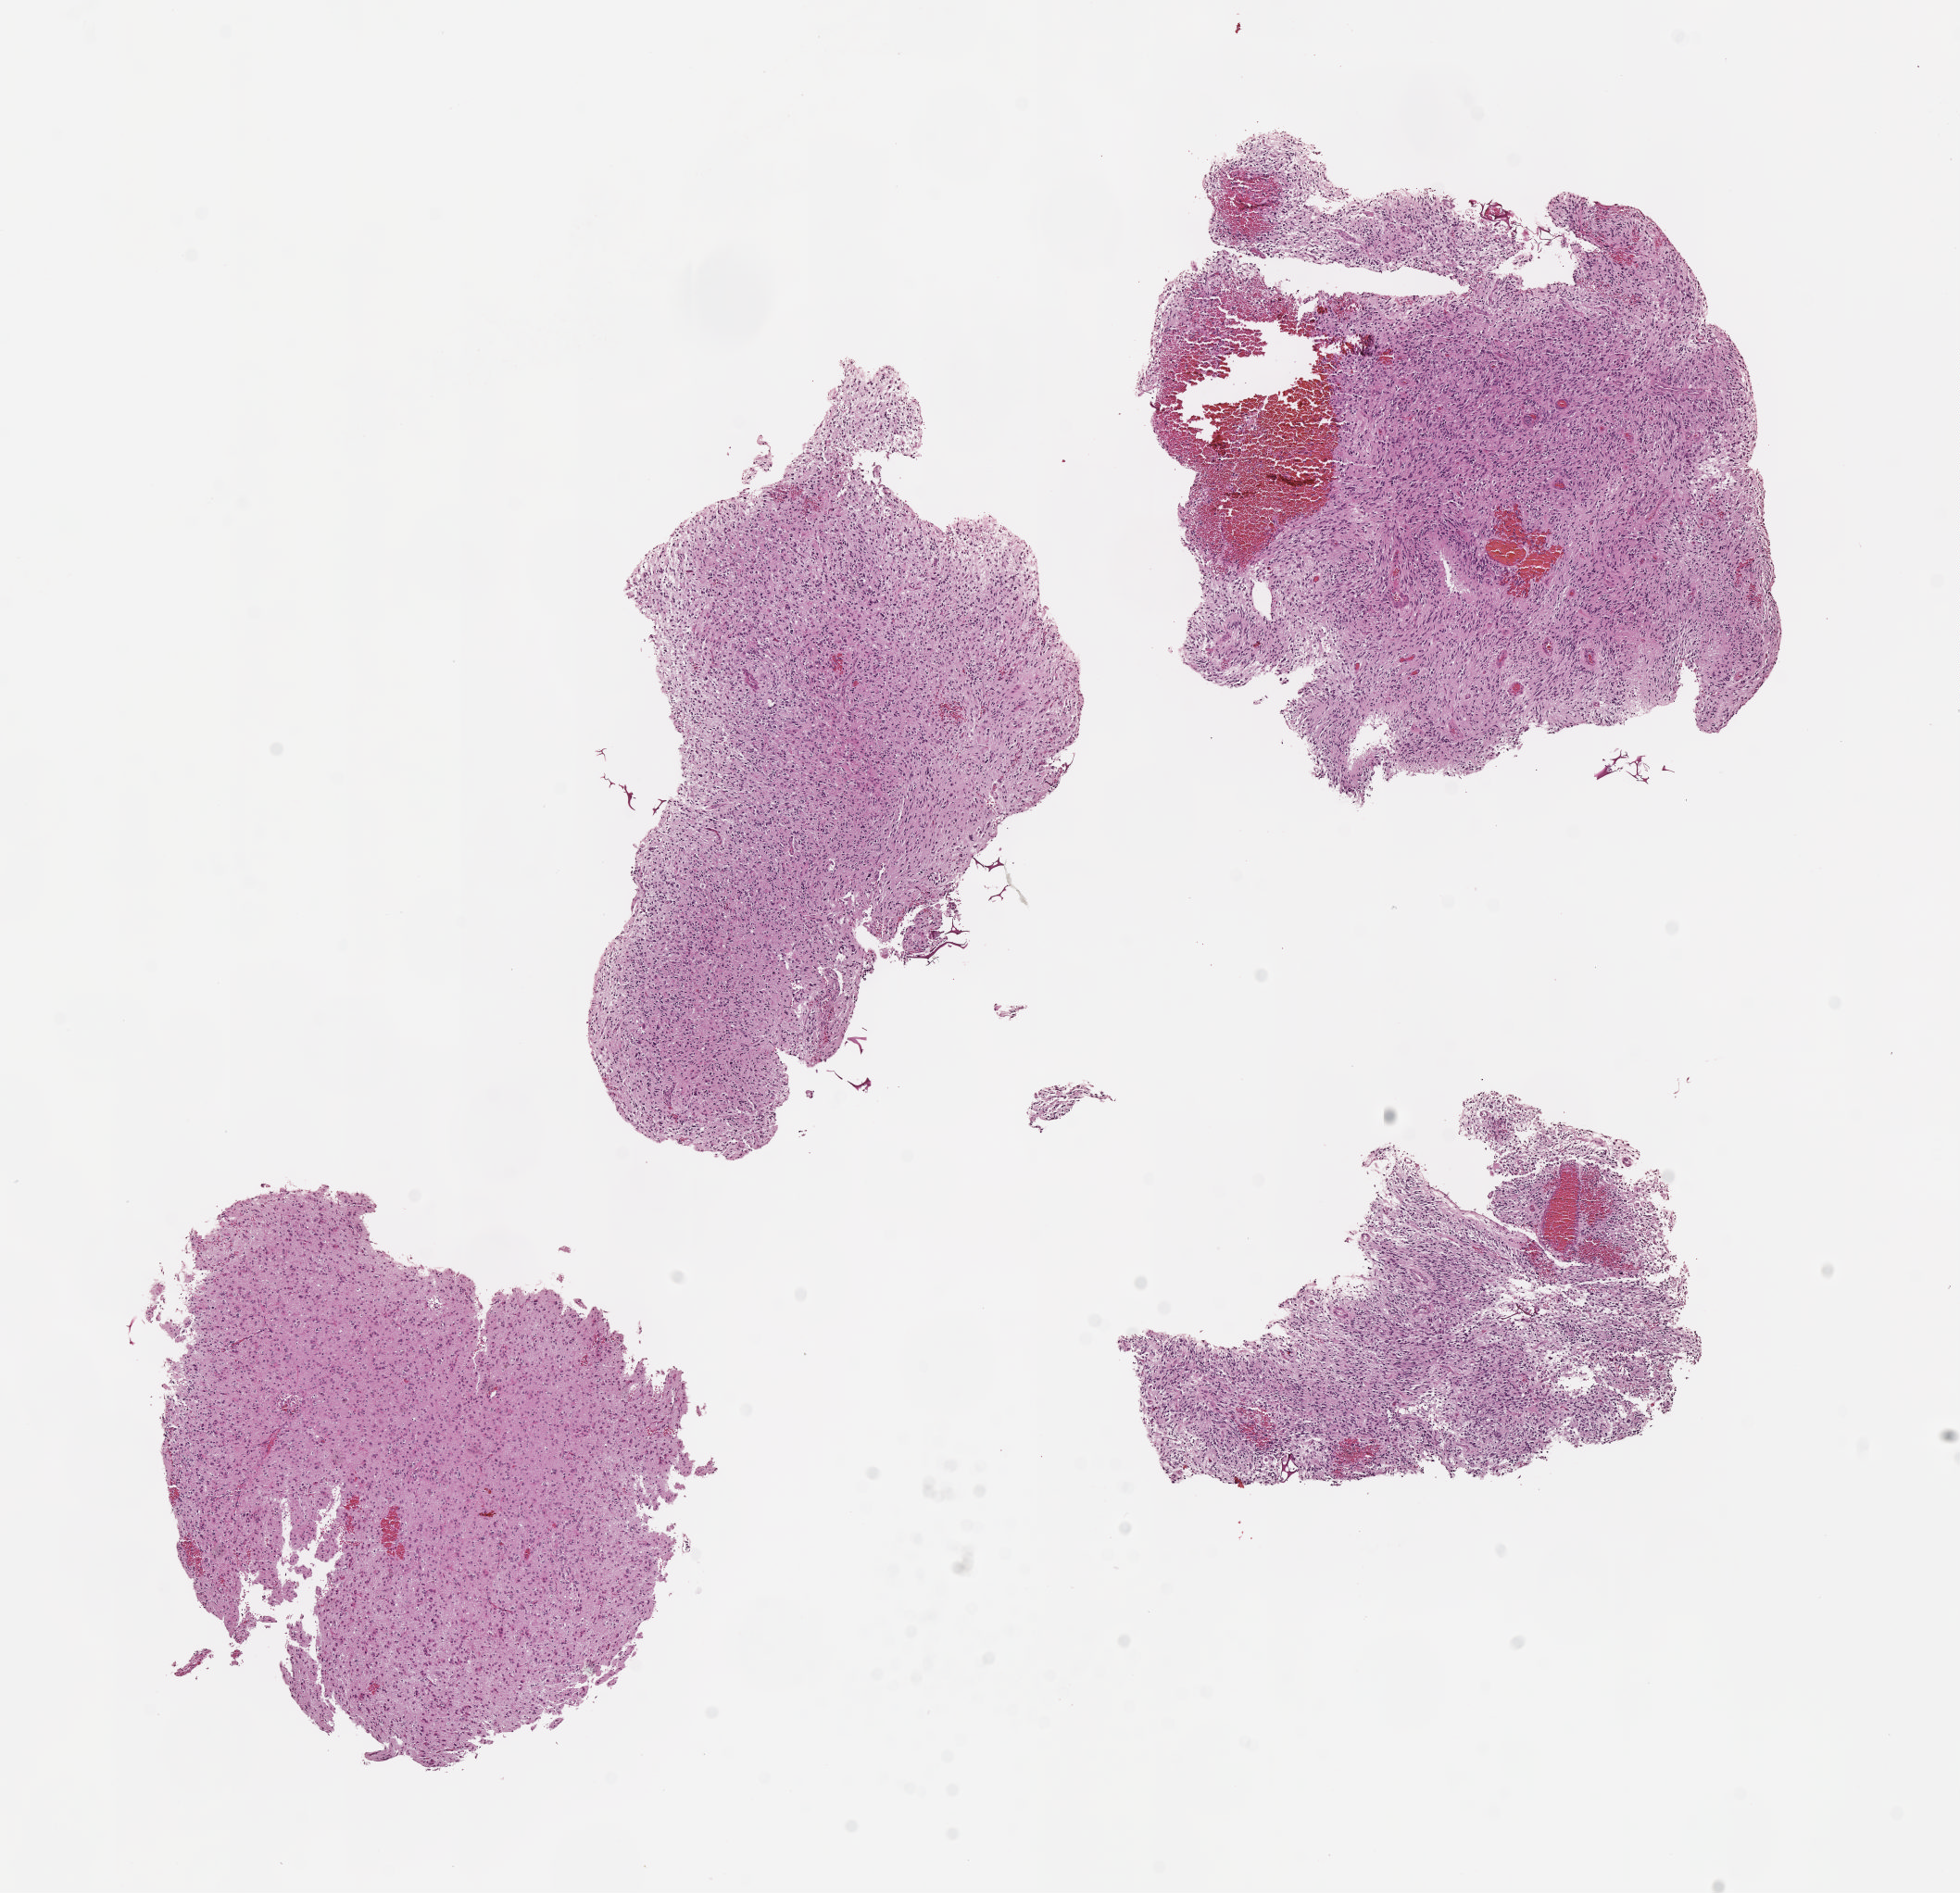
Digitized H&E-stained tissue section (whole slide), a low-resolution overview of the entire scanned area, about 8.6 x 8.3 mm; formalin-fixed paraffin-embedded (FFPE) diagnostic section; sample: primary tumour, brain. Patient: male, age at initial diagnosis 70 years. Histologic grade: G3 (poorly differentiated).
Histologic diagnosis: Oligodendroglioma, anaplastic (cerebrum).